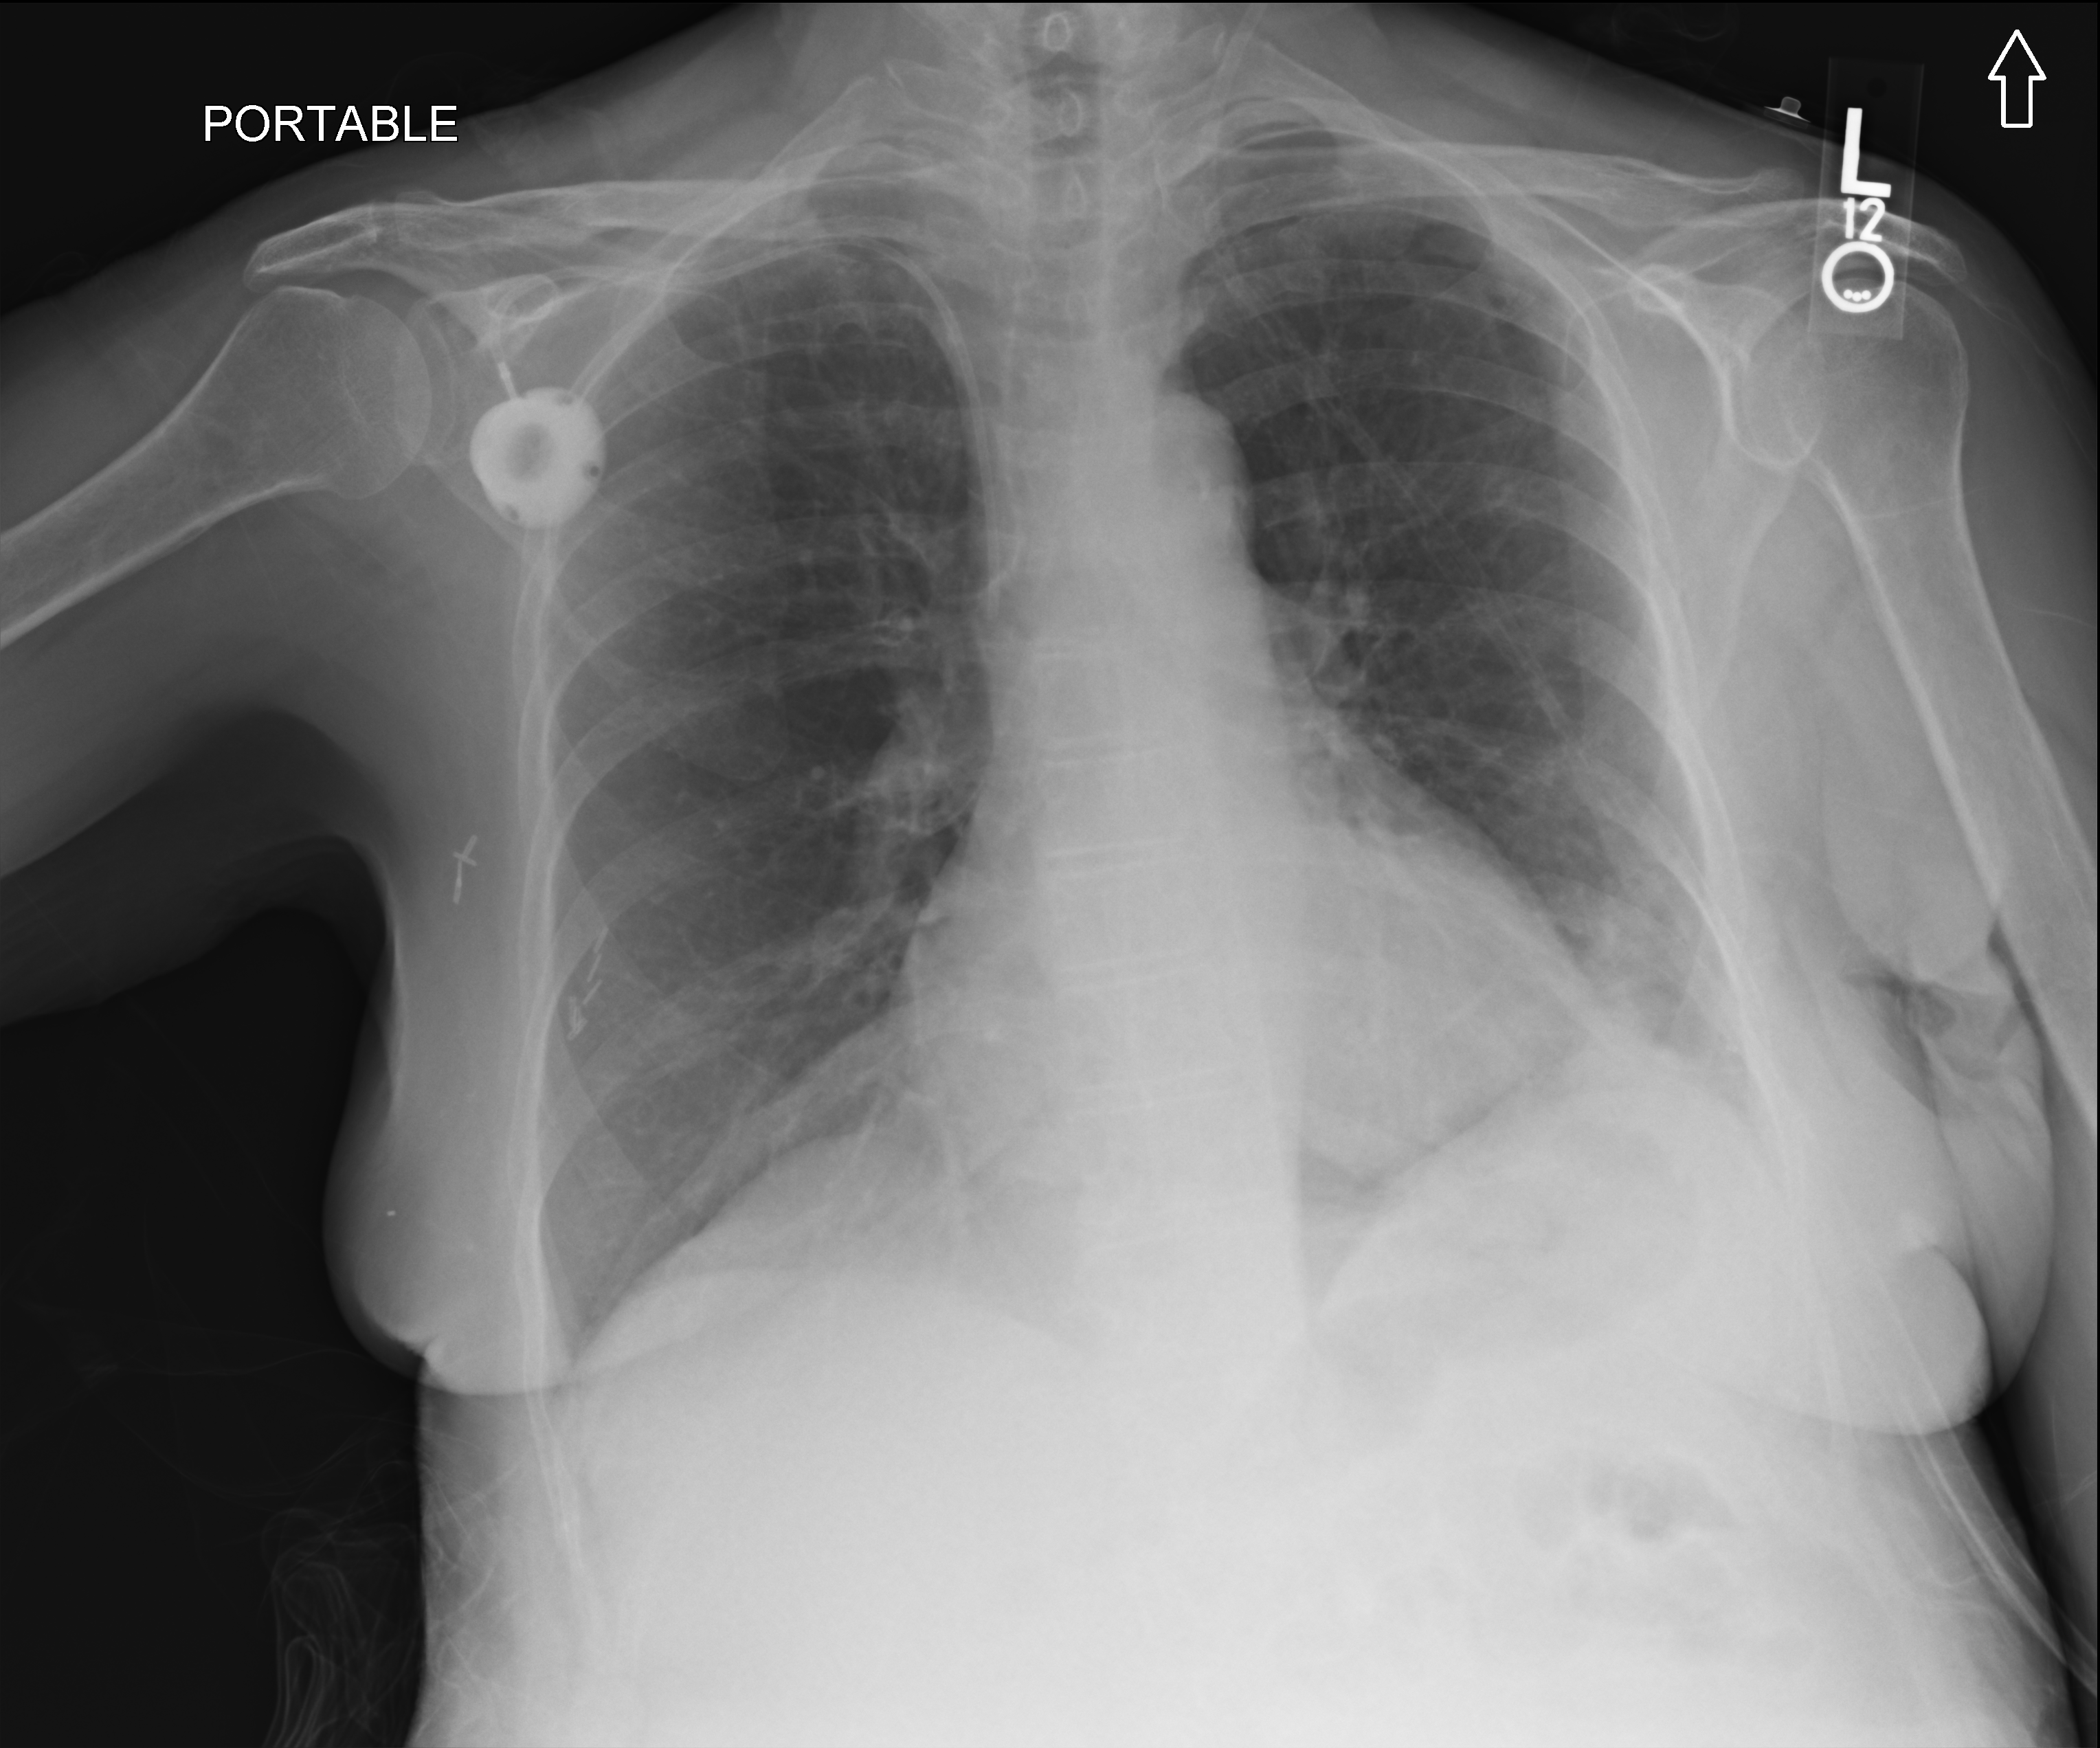
Chest X-ray (portable), anteroposterior (AP) projection. Patient hospitalised with COVID-19; female, aged 60–74 years.
Hospital-stay facts (about this admission, not read from this image; timing relative to this image not recorded): mechanically ventilated during this hospital stay: yes.